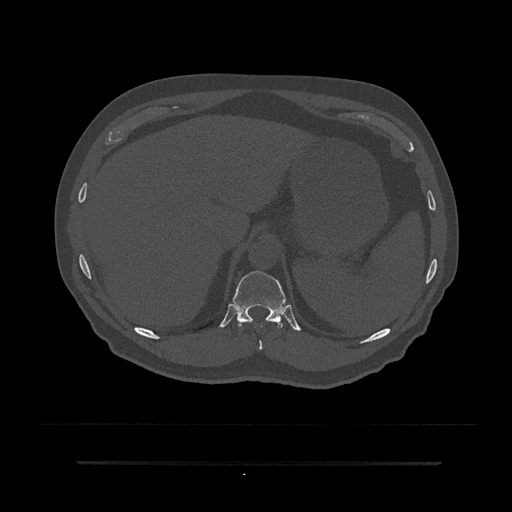
CT including the spine, one axial slice. Slice 288 of 797 in the series (ordered by position). Reconstruction kernel Br40s/3. Bone window (W 1800 / L 400 HU). 0.5 mm slice thickness. 512 × 512 image matrix. Patient: male, 59 years. Case-level facts recorded for this patient, not image findings: primary cancer: bile ducts.
Outlined on this slice (semi-automatically segmented with operator editing):
- T10 vertebra: box from (x=241, y=321) to (x=270, y=351) px
- T11 vertebra: (x=232, y=271)–(x=289, y=328)